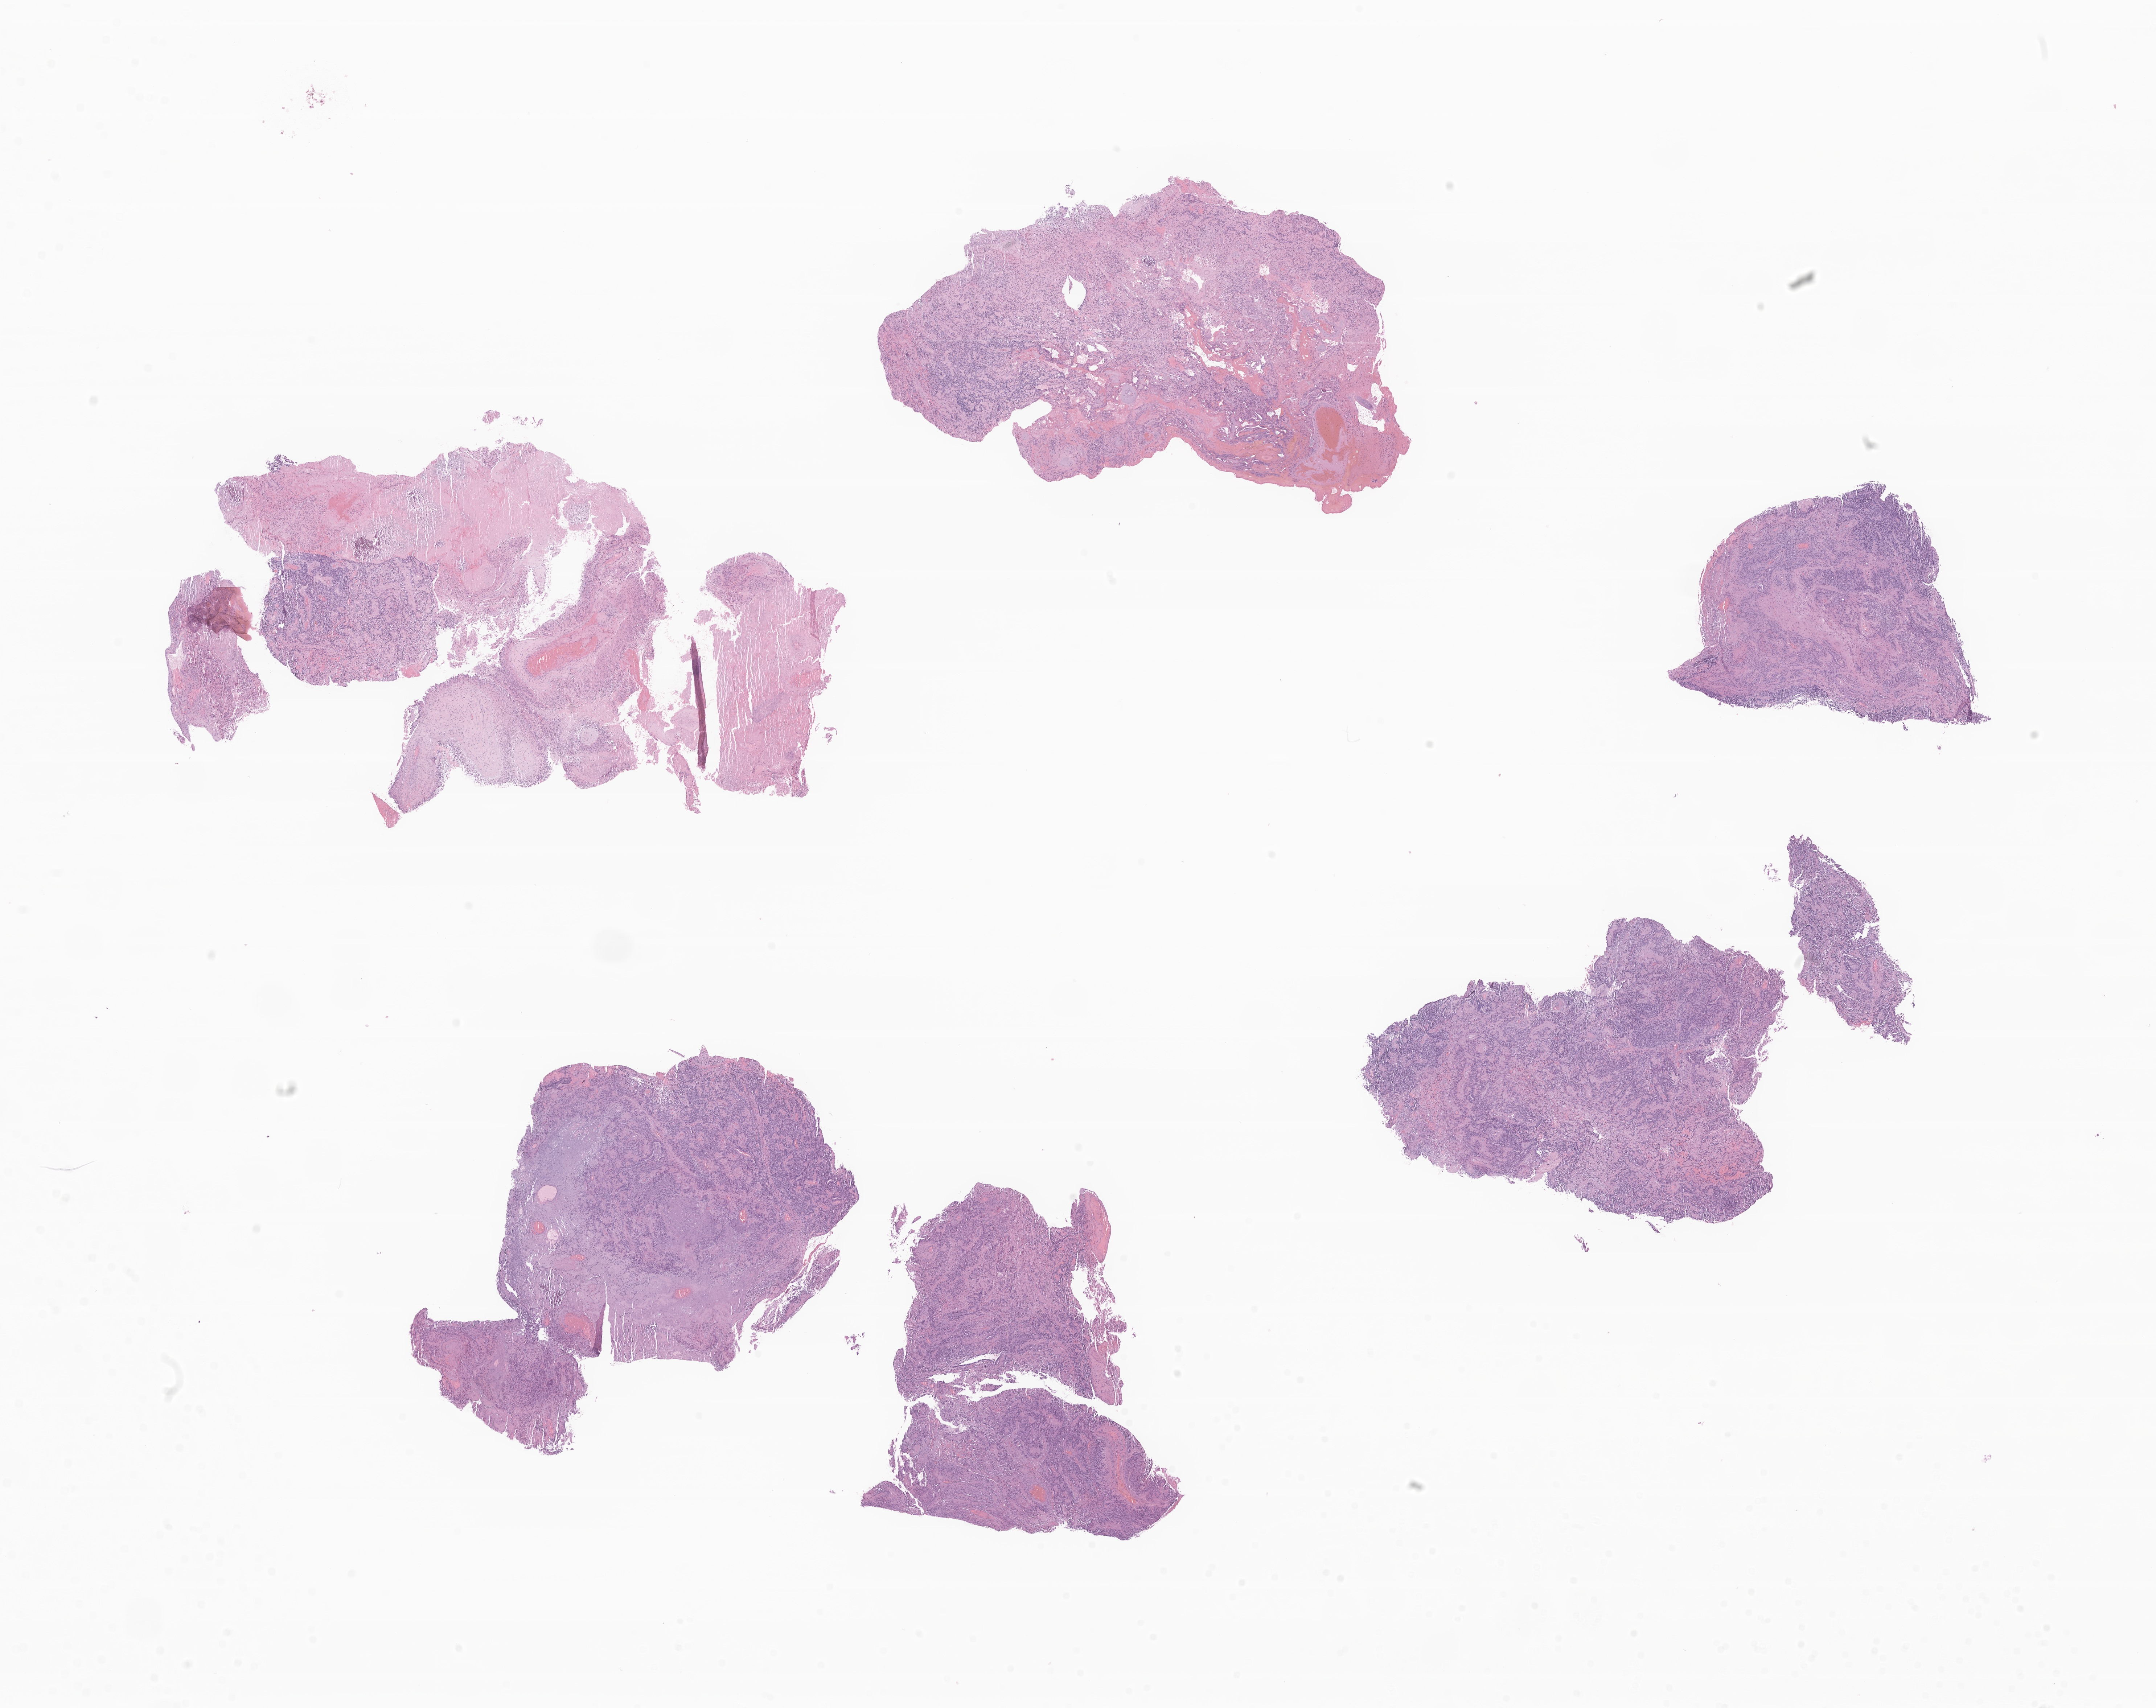
Digitized hematoxylin and eosin (H&E)-stained section of tumor tissue from the brain, low-resolution overview of the scanned area, about 25.1 x 19.9 mm; FFPE section. Patient male; age 125 months (10 years 5 months).
* diagnosis (ICD-O-3 morphology term): Ependymoma, anaplastic